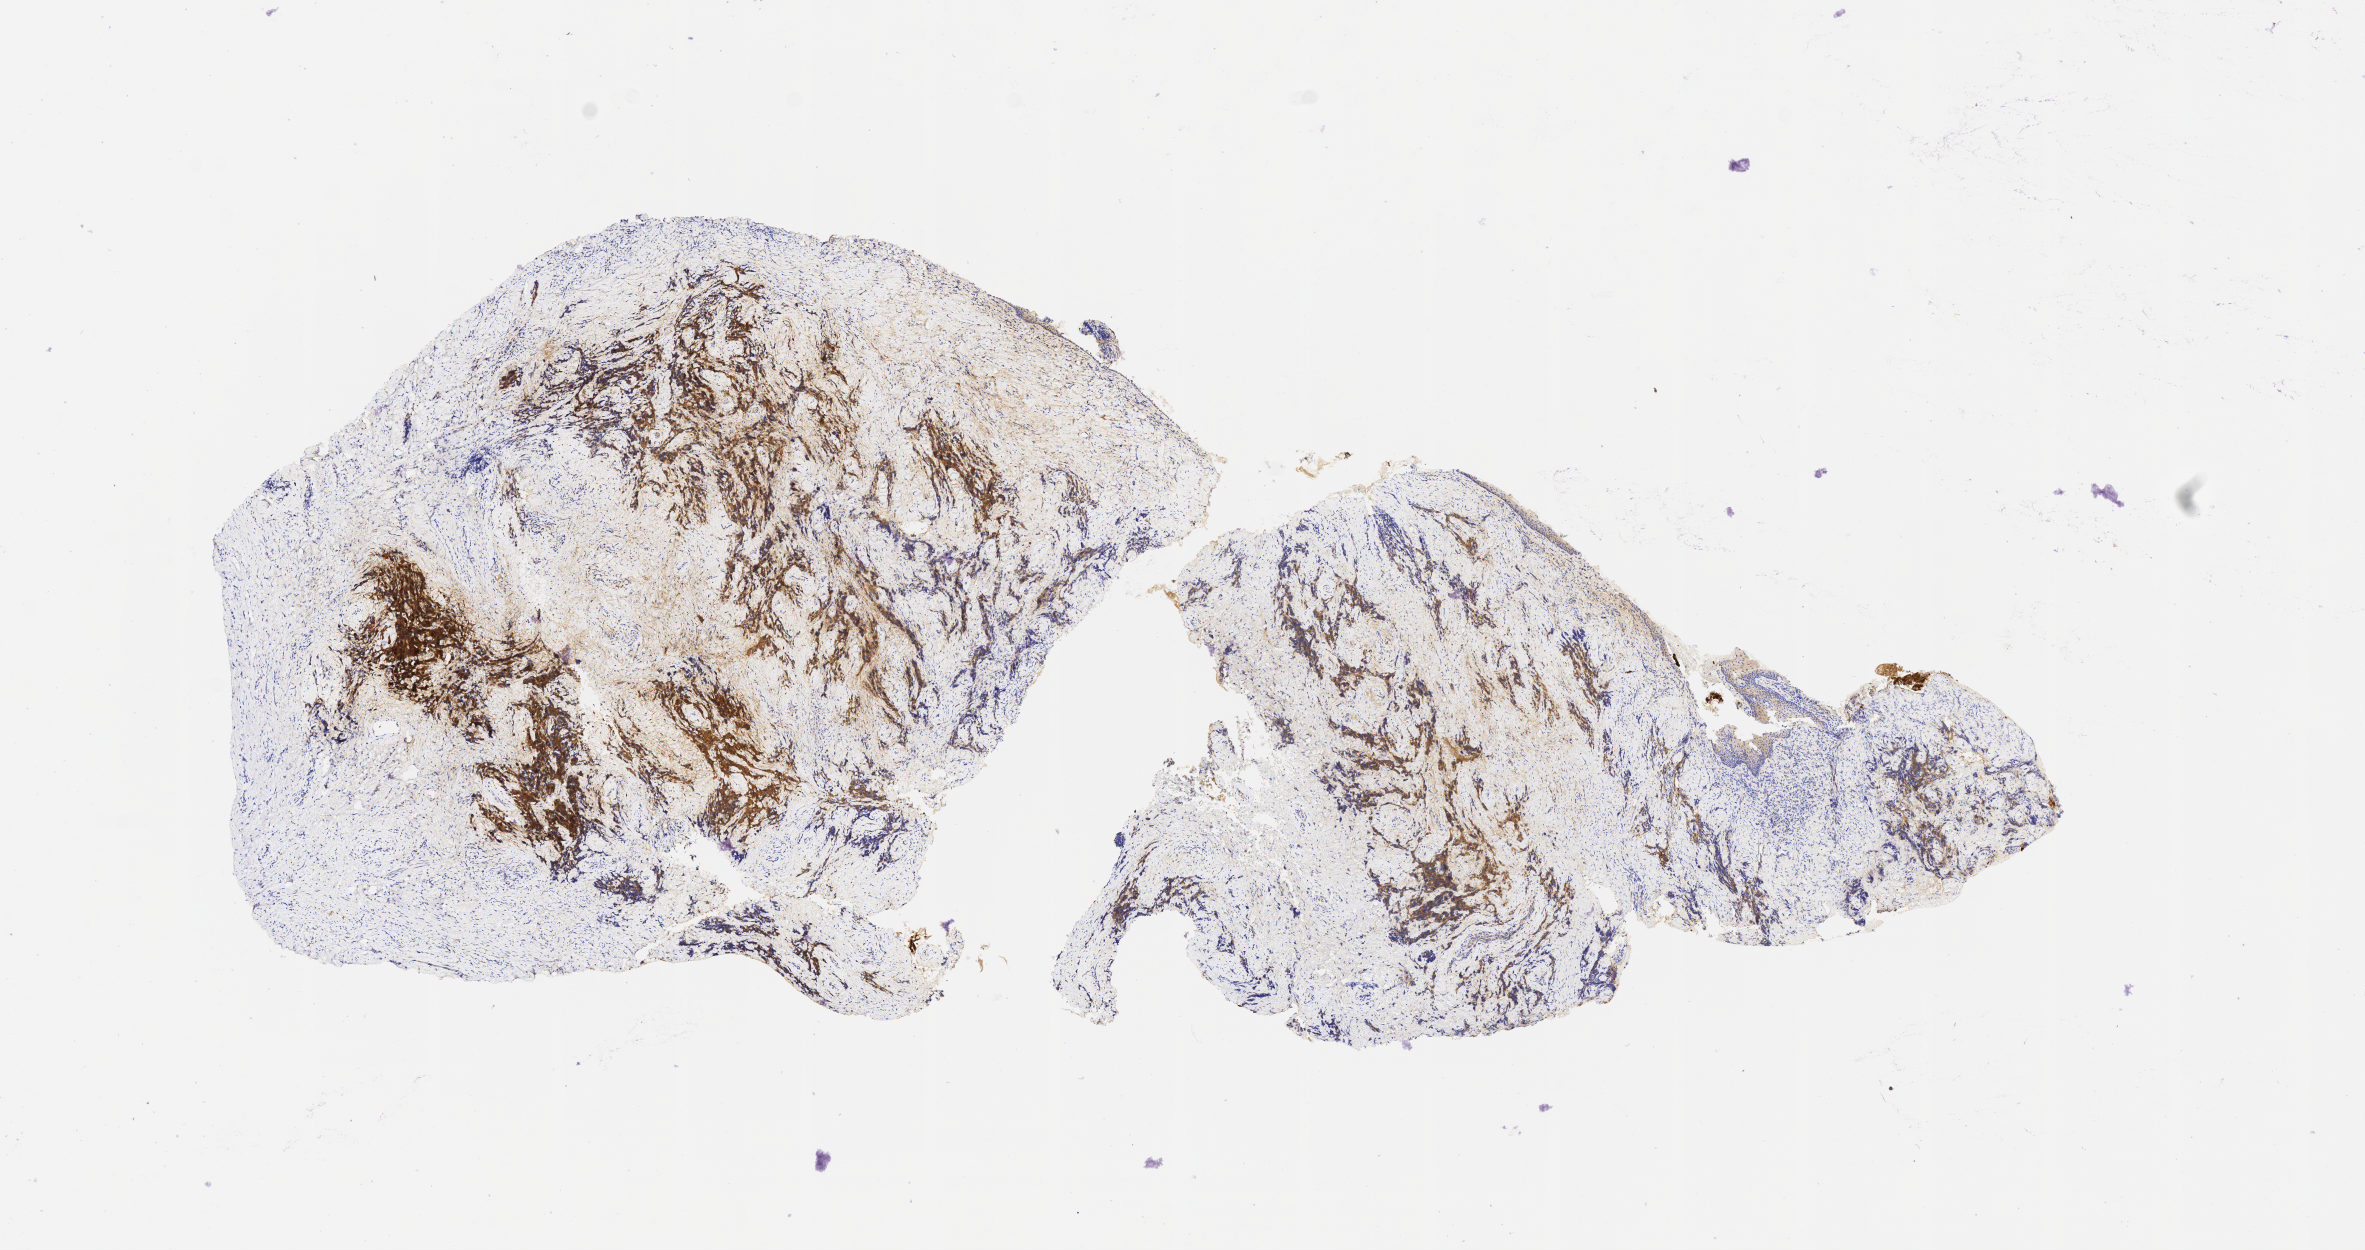
IHC for p16 (p16INK4a), whole-slide image — shown as a low-resolution overview of the whole scanned area (about 9.6 x 5.1 mm), tumor tissue, site: cervix. Patient female; aged 59.
Histologic diagnosis: Small cell carcinoma, NOS.